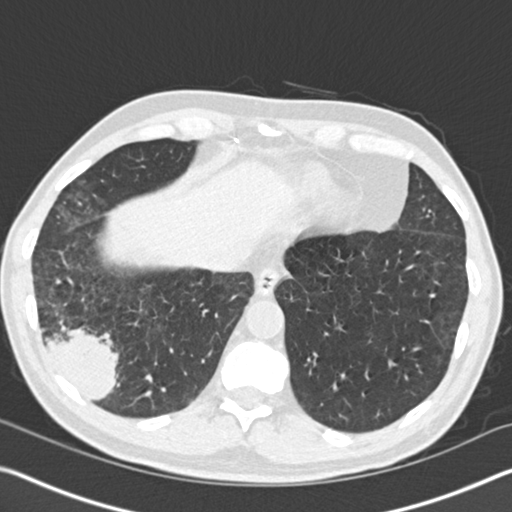
Axial slice from a low-dose chest CT screening exam, first (baseline) screen, lung window (W 1500 / L -600 HU), 2 mm slice thickness, standard (soft-tissue) reconstruction kernel (B30f), 120 kVp. Male, age 61 years at enrolment.
Lesion marked by an expert reader, bounding box (x1, y1, x2, y2) in pixels: (16, 282, 140, 415). The exam's reader record, not a measurement of the box and not confirmed to be the same lesion: non-calcified nodule or mass ≥4 mm, right lower lobe, 52 × 36 mm, spiculated (stellate) margins, soft tissue attenuation. Official screen result: positive, change unspecified: nodule(s) >= 4 mm or enlarging nodule(s), mass(es), or other non-specific abnormalities suspicious for lung cancer. Later outcome: lung cancer diagnosed 392 days after this screen — bronchiolo-alveolar adenocarcinoma, NOS, right lower lobe, moderately differentiated (G2), stage IIIB (AJCC 6th edition), 90 mm at pathology.